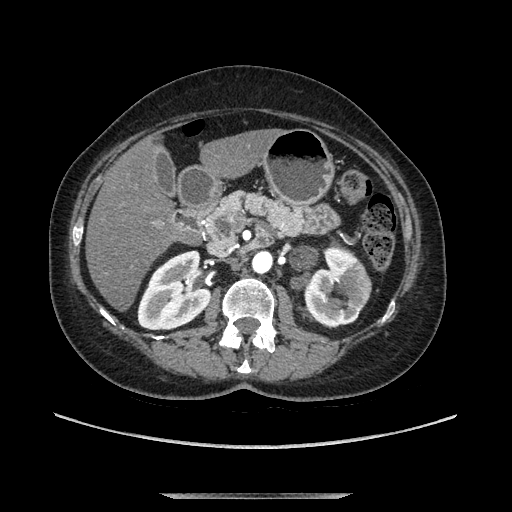
Contrast-enhanced abdominal CT, one axial slice. Position 54 of 169 along the scan axis. Soft-tissue window (W 400 / L 40 HU). 1.25 mm slice thickness. 512 × 512 image matrix. Female patient. From the clinical record (not read from this slice): diagnosis: adrenocortical carcinoma; tumour side: left adrenal; tumour size at pathology: 9 cm; Ki-67 index: 2 %.
Structures marked on this image (semi-automatically segmented with operator editing):
- mass: bounding box (x1, y1, x2, y2) in pixels: (292, 250, 316, 270)